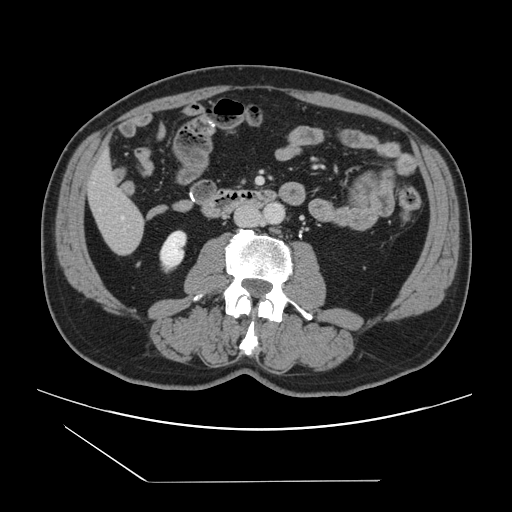
Contrast-enhanced abdominal CT, one axial slice. Slice 26 of 157 in the series (ordered by position). 120 kVp. Intravenous contrast given. Soft-tissue window (W 400 / L 40 HU). 2.5 mm slice thickness. 512 × 512 image matrix, field of view 407 × 407 mm. Male patient, age 61 years. From the clinical record (not read from this slice): diagnosis: colorectal cancer liver metastases, imaged before liver resection; multiple liver metastases: yes; largest metastasis: 5.5 cm; disease in both lobes: yes.
Annotated regions visible in this slice (manually delineated by an expert):
- liver: box from (x=90, y=157) to (x=144, y=254) px
- planned liver remnant (the part of the liver to remain after resection): (x=89, y=156)–(x=137, y=218)